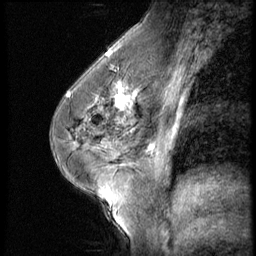
Breast MRI (dynamic contrast-enhanced), one sagittal slice; position 31 of 56 along the scan axis; 3 images stored at this slice position (order not interpretable as contrast timing); 1.5 T; TE 4.2 ms, TR 9 ms; 2.5 mm slice thickness; 256 × 256 image matrix, field of view 180 × 180 mm. Female patient, age 45 years. From the clinical record (not read from this slice): setting: breast cancer imaged before/during neoadjuvant chemotherapy; receptor status: HR-positive, HER2-negative.
Outlined on this slice (semi-automatically segmented with operator editing):
- analysis volume of interest (the breast-tissue region the enhancement analysis was run in; not a lesion): bounding box [x1, y1, x2, y2] px = [102, 77, 166, 129]
- tumour enhancement mask (voxels above the 140 % enhancement threshold inside the analysis volume of interest): [114, 80, 147, 125]